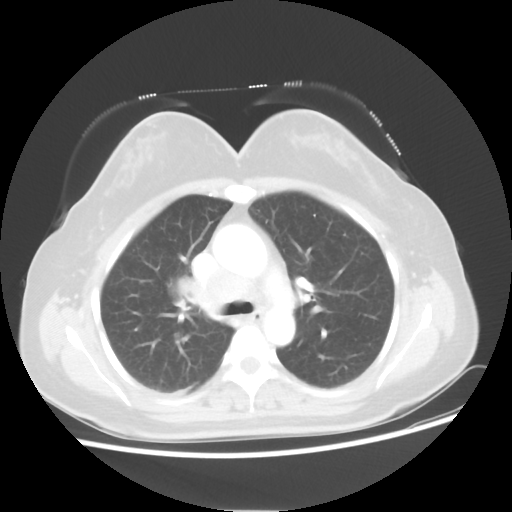
Chest CT, one axial slice; reconstruction kernel STANDARD; 100 kVp; lung window (W 1500 / L -600 HU); 5 mm slice thickness; 512 × 512 image matrix, field of view 360 × 360 mm. Patient: female, 40 years. From the clinical record (not read from this slice): clinical TNM (as recorded): T1c N3 M0; histopathological grade: G3.
Structures marked on this image (bounding box drawn by a radiologist):
- lung tumour (recorded histology: small cell carcinoma): bounding box <180,276,204,316> (left, top, right, bottom; pixels)